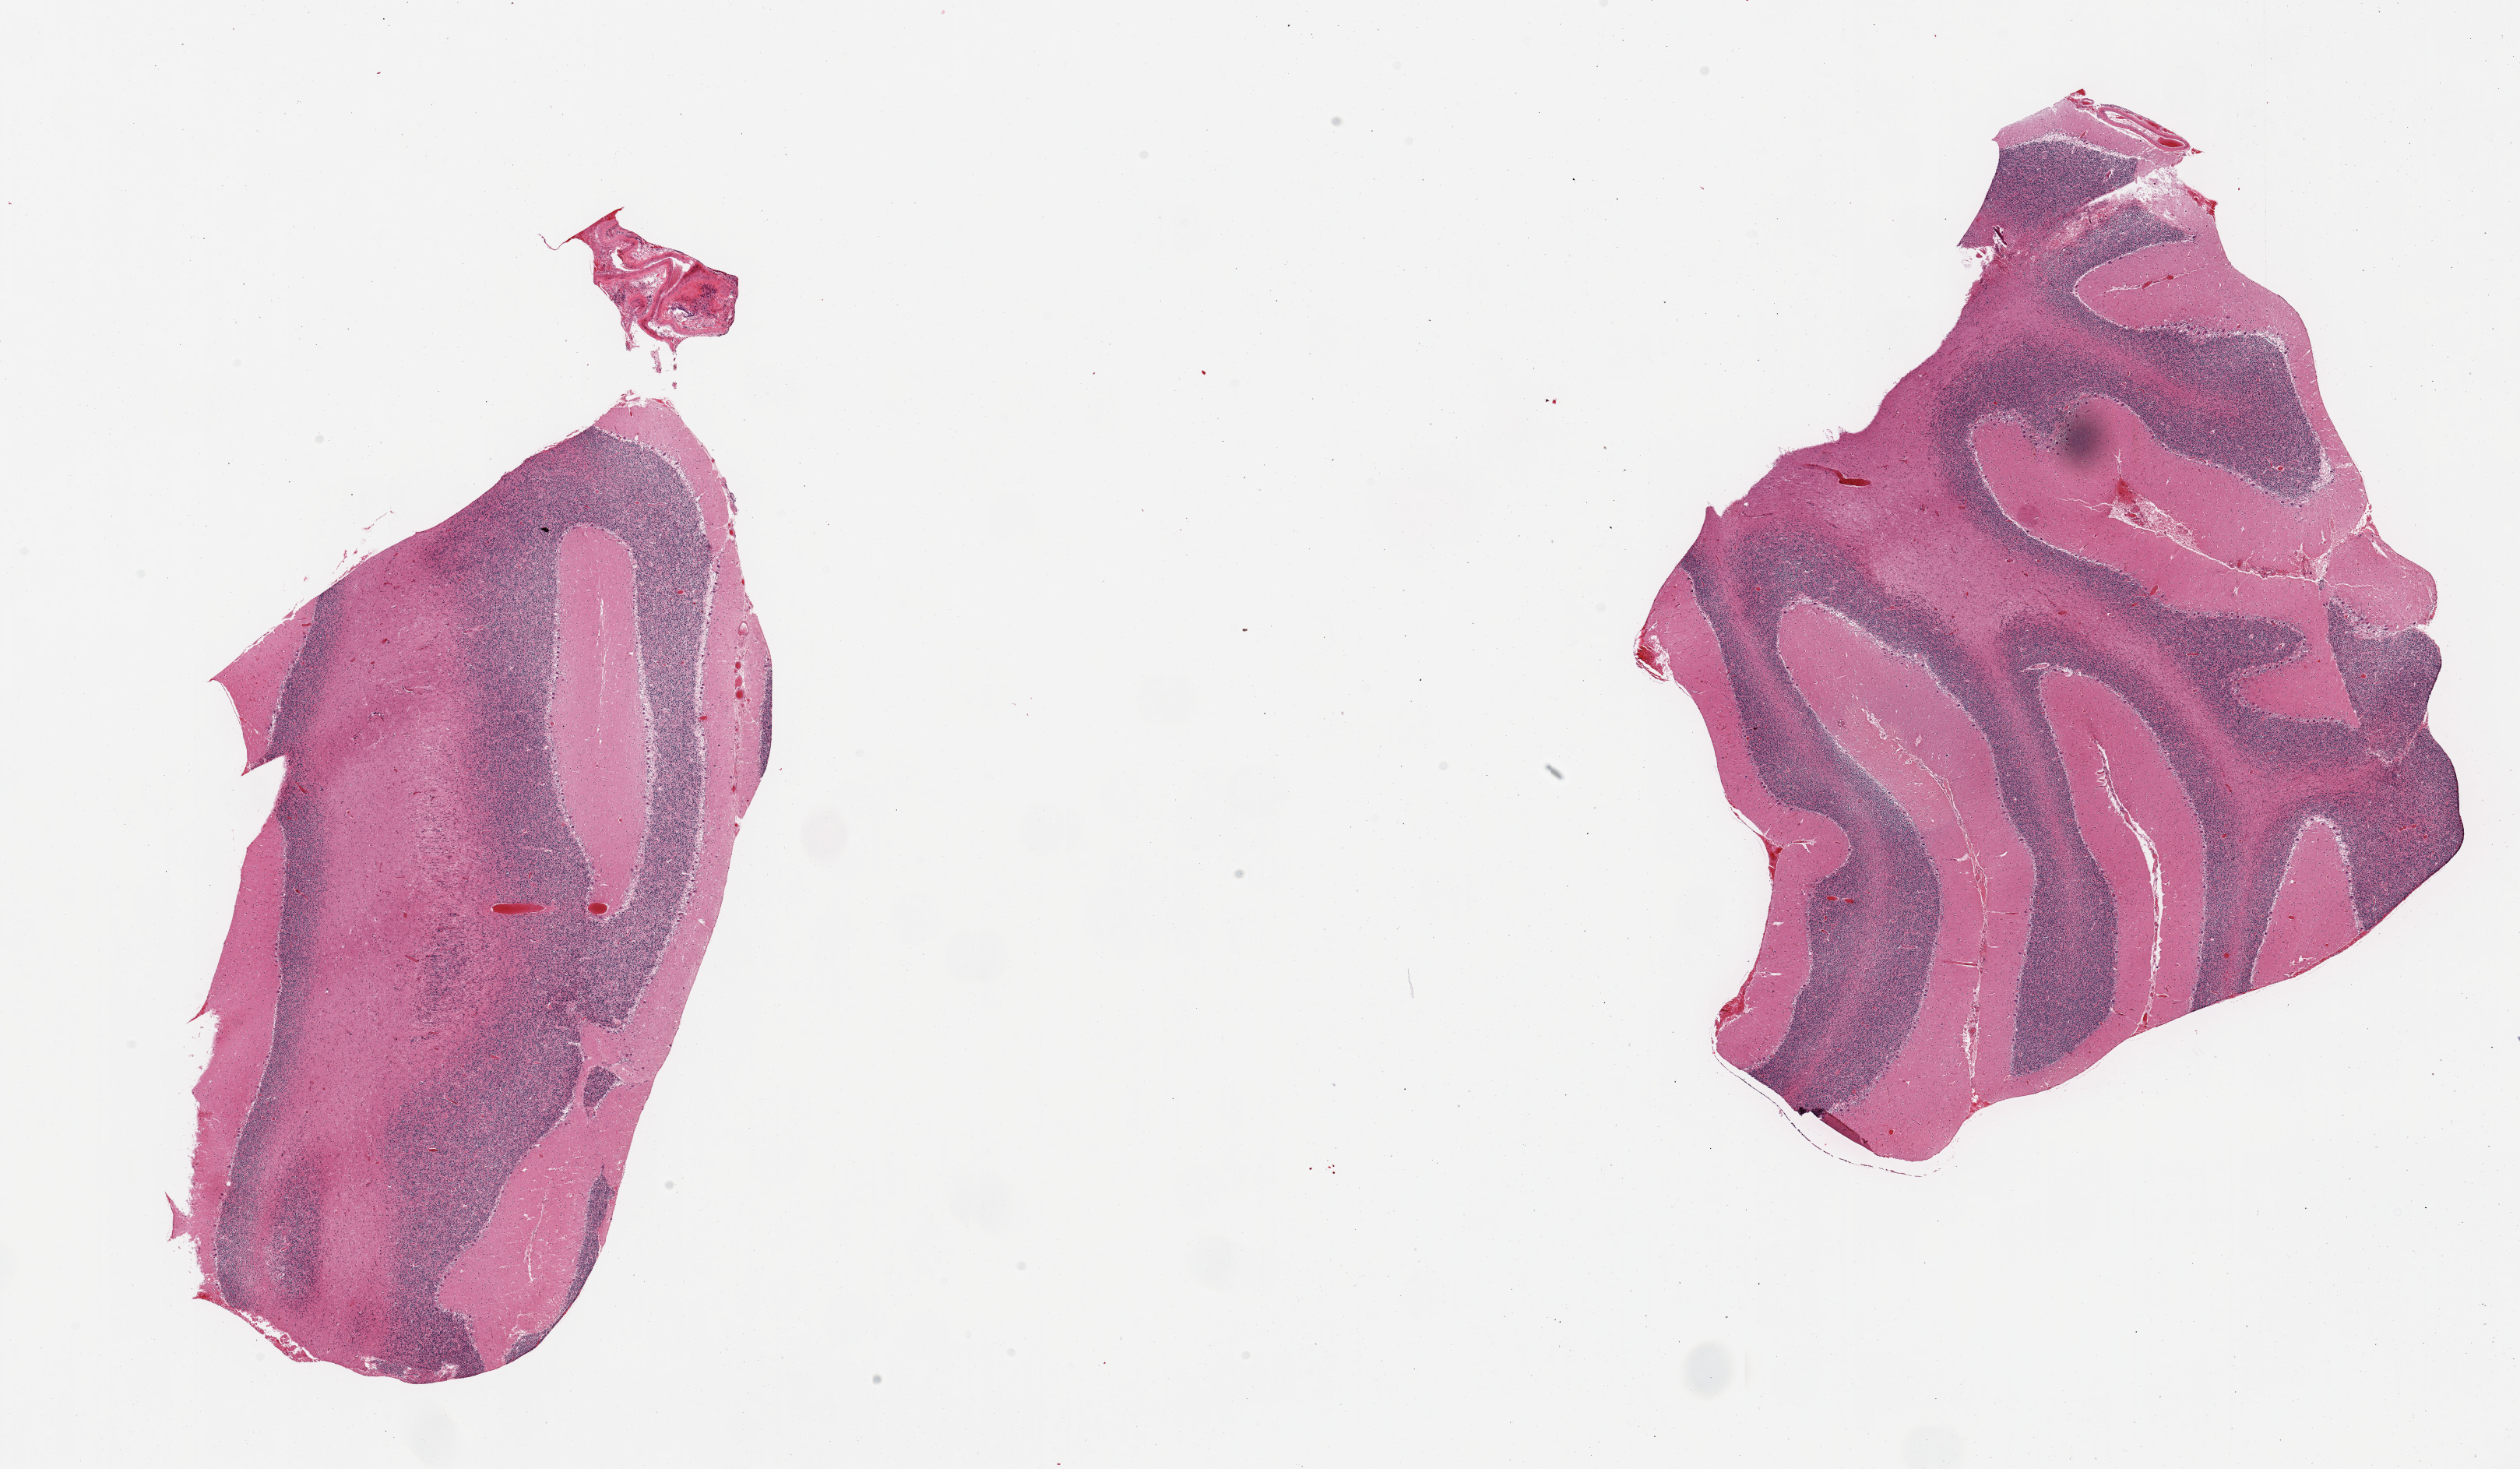
Haematoxylin and eosin whole-slide image, low-resolution overview of the scanned area, about 25.6 x 14.9 mm, PAXgene-fixed, paraffin-embedded tissue, sampled site (target tissue): cerebellum, donor tissue sample. Donor: male.
- reviewer comment on this tissue sample: 2 pieces